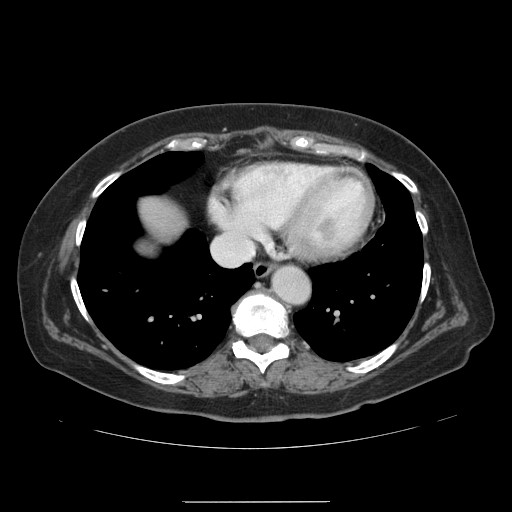
Contrast-enhanced abdominal CT, one axial slice; position 130 of 141 along the scan axis; intravenous contrast given; soft-tissue window (W 400 / L 40 HU); 512 × 512 image matrix, field of view 393 × 393 mm. Female patient, age 74 years. From the clinical record (not read from this slice): diagnosis: colorectal cancer liver metastases, imaged before liver resection.
Outlined on this slice (outlined manually by an expert reader):
- liver: bounding box (x1, y1, x2, y2) in pixels: (141, 201, 181, 233)
- planned liver remnant (the part of the liver to remain after resection): (141, 201, 163, 233)